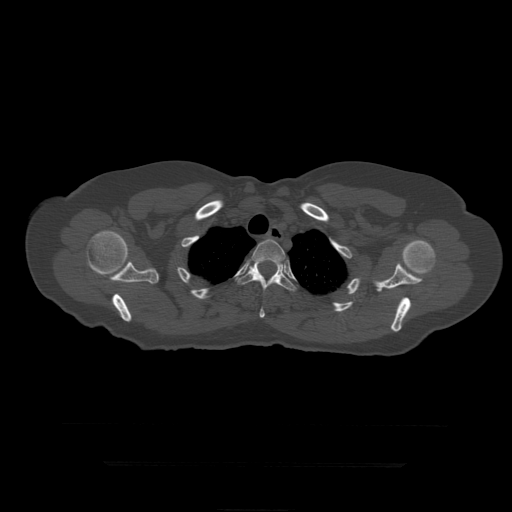
CT including the spine, one axial slice. Slice 355 of 399 in the series (ordered by position). Reconstruction kernel STANDARD. 120 kVp. Bone window (W 1800 / L 400 HU). 1.25 mm slice thickness. 512 × 512 image matrix. Patient age 41 years. From the clinical record (not read from this slice): primary cancer: breast.
Structures marked on this image (semi-automatically segmented with operator editing):
- T3 vertebra: box from (x=249, y=239) to (x=286, y=269) px
- T4 vertebra: (x=238, y=262)–(x=297, y=318)